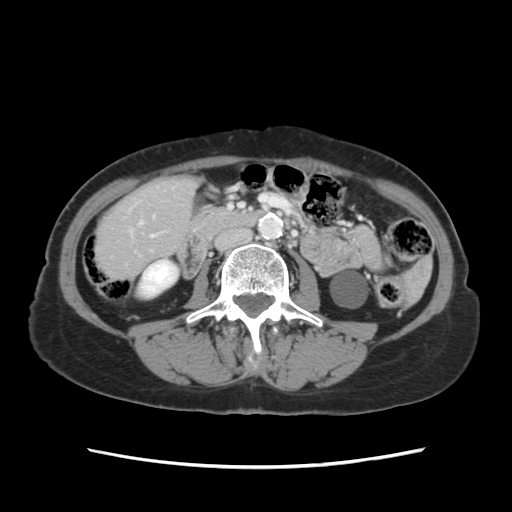
Contrast-enhanced abdominal CT, one axial slice; position 22 of 120 along the scan axis; 120 kVp; soft-tissue window (W 400 / L 40 HU); 2.5 mm slice thickness; 512 × 512 image matrix, field of view 330 × 330 mm. Female patient, age 70 years. Case-level facts recorded for this patient, not image findings: diagnosis: colorectal cancer liver metastases, imaged before liver resection; multiple liver metastases: no; largest metastasis: 2.5 cm; chemotherapy before resection: yes.
Annotated regions visible in this slice (manually delineated by an expert):
- liver: bounding box [x1, y1, x2, y2] px = [97, 178, 194, 277]
- planned liver remnant (the part of the liver to remain after resection): [98, 179, 193, 277]